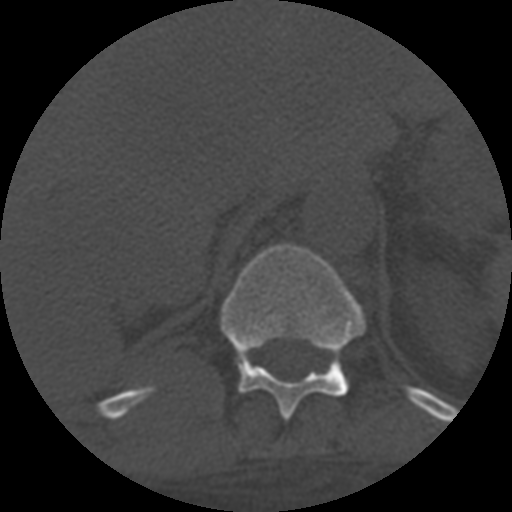
CT including the spine, one axial slice; slice 334 of 708 in the series (ordered by position); 120 kVp; one of 3 acquisitions stored at this slice position; bone window (W 1800 / L 400 HU); 512 × 512 image matrix, field of view 160 × 160 mm. Patient age 55 years. From the clinical record (not read from this slice): primary cancer: colon; vertebrae with lytic lesions (as recorded): T12, L1, L5.
Structures marked on this image (semi-automatic segmentation, software-assisted and operator-edited):
- T11 vertebra: bounding box (x1, y1, x2, y2) in pixels: (209, 244, 367, 420)